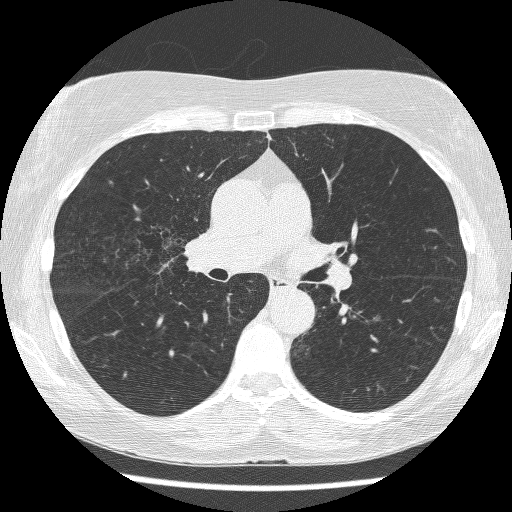
Axial slice from a low-dose chest CT screening exam; baseline annual screen; lung window (W 1500 / L -600 HU); 1.25 mm slice thickness; lung (sharp) reconstruction kernel (BONE); 120 kVp; 512 × 512 image matrix. Female participant, aged 64 years at enrolment.
• Lesion marked by an expert reader, bounding box (x1, y1, x2, y2) in pixels: (121, 212, 196, 270).
• The screening reader recorded 3 non-calcified nodules or masses ≥4 mm on this exam (right upper lobe, right upper lobe, left lower lobe); which of them this box marks is not recorded.